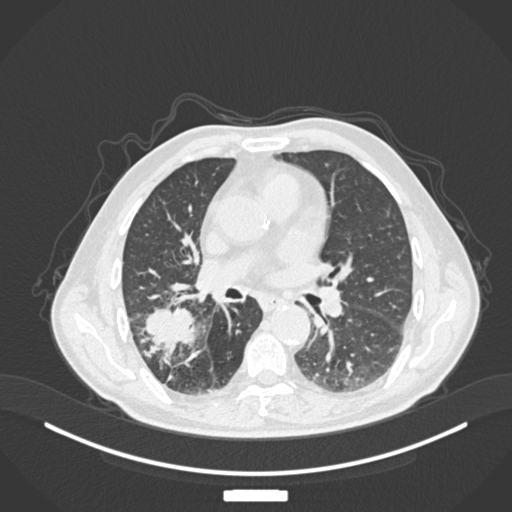
Chest CT, one axial slice. 120 kVp. Lung window (W 1500 / L -600 HU). 512 × 512 image matrix. Patient: male, 72 years. From the clinical record (not read from this slice): clinical TNM (as recorded): T3 N2 M0.
Outlined on this slice (rectangle marked by the reading radiologist):
- lung tumour (recorded histology: adenocarcinoma): bounding box (x1, y1, x2, y2) in pixels: (140, 305, 203, 355)